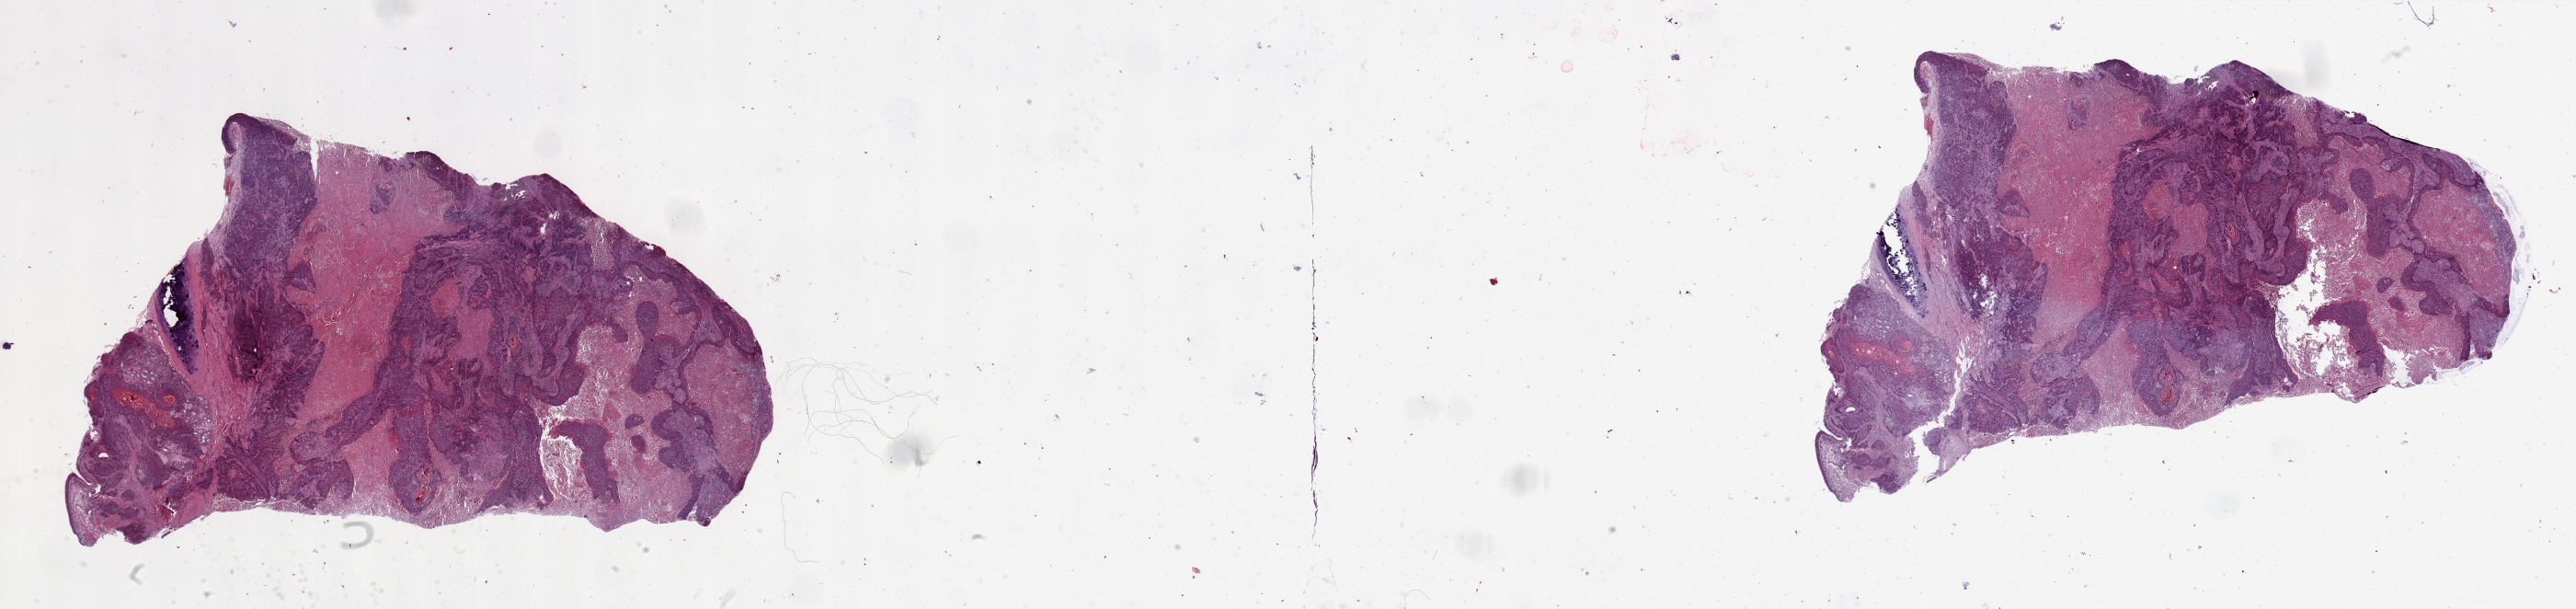
Digitized H&E-stained tissue section (whole slide) — shown as a low-resolution overview of the whole scanned area (about 44.3 x 10.5 mm, from a 20x scan). Tumour tissue sample, lung. Patient: male, age 57 years. Histologic grade: G2 (moderately differentiated).
- primary tumour site (as recorded): left upper lobe
- histologic diagnosis: Squamous cell carcinoma, NOS
- AJCC pathologic stage: IIA